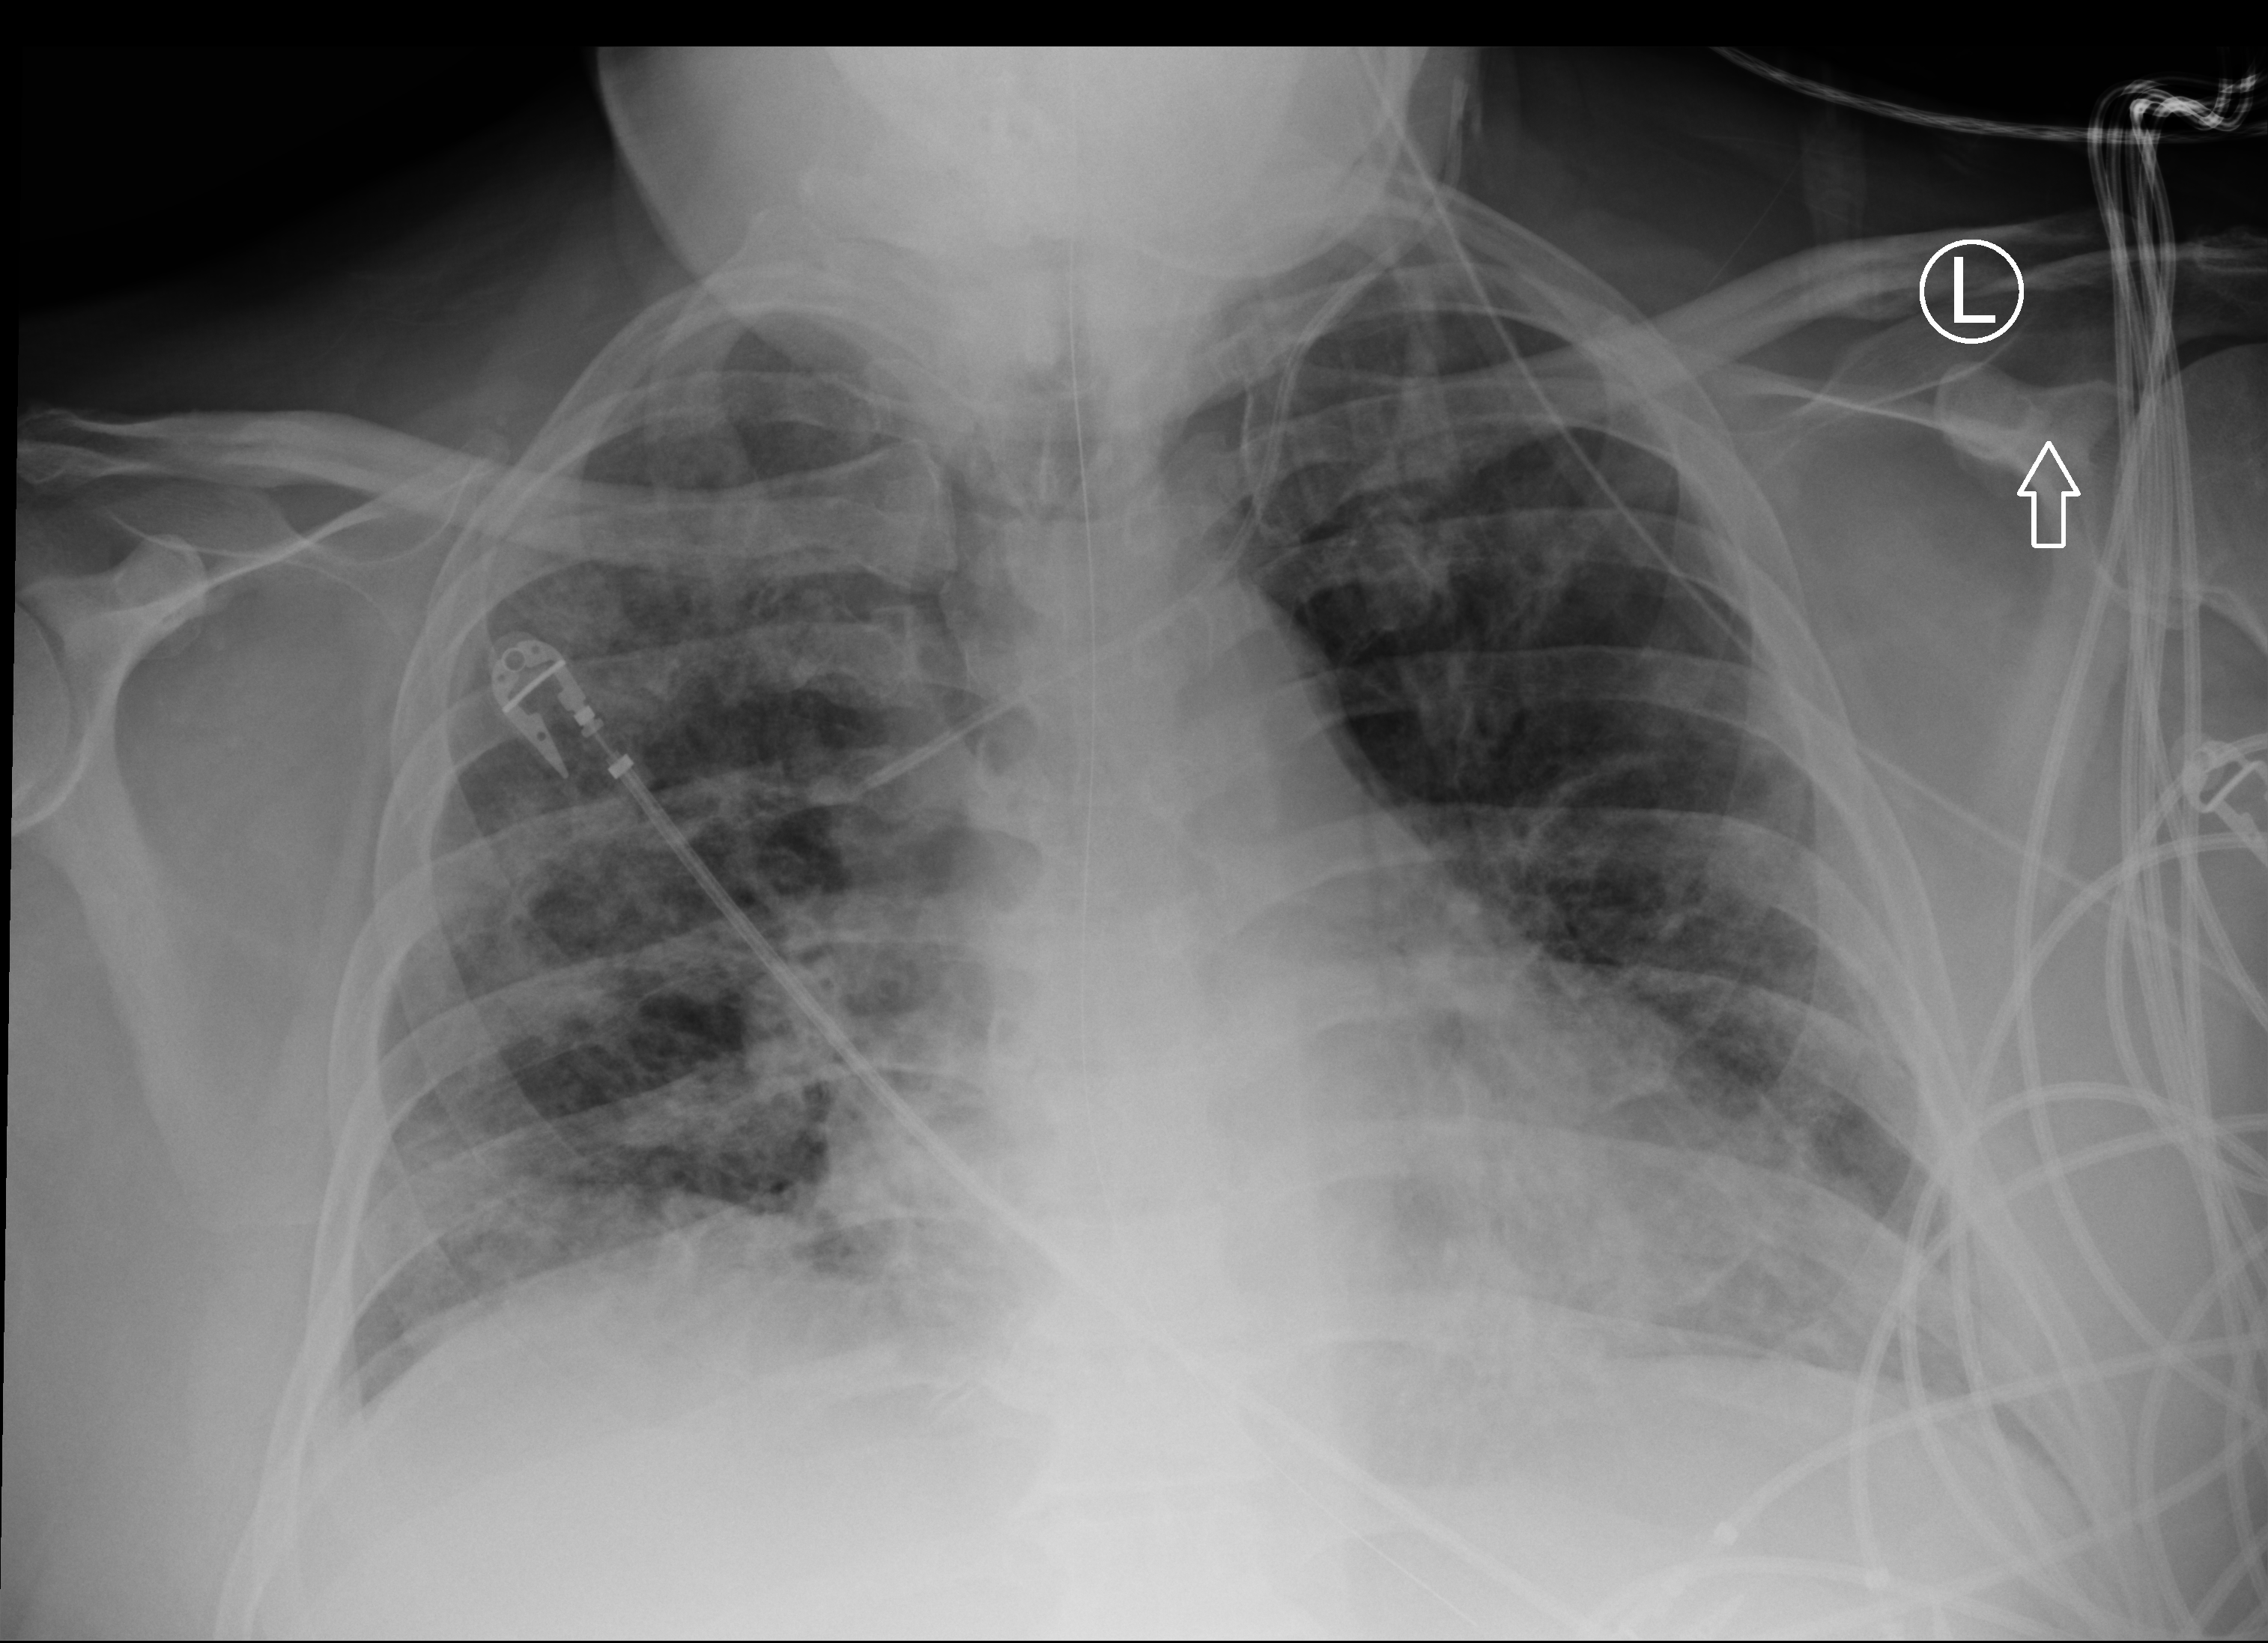
Bedside chest radiograph (computed radiography); anteroposterior (AP) projection. Patient hospitalised with COVID-19; male, aged 18–59 years.
Admission-level facts for this patient (not findings on this image; timing relative to this image not recorded): length of hospital stay: 47 days; mechanically ventilated during this hospital stay: yes; admitted to intensive care during this hospital stay: yes.